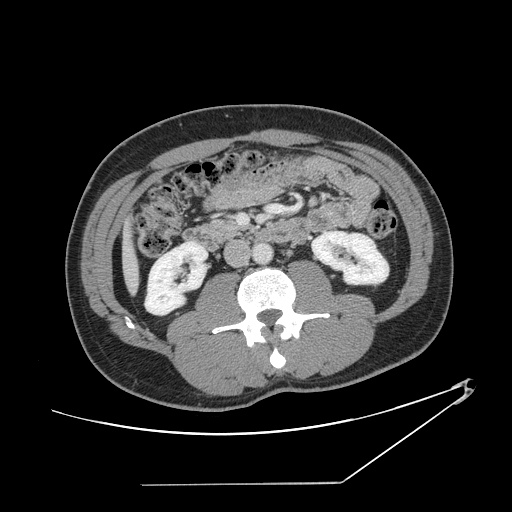
Contrast-enhanced abdominal CT, one axial slice; slice 43 of 152 in the series (ordered by position); reconstruction kernel STANDARD; intravenous contrast given; soft-tissue window (W 400 / L 40 HU); 2.5 mm slice thickness; 512 × 512 image matrix, field of view 432 × 432 mm. Male patient, age 45 years. Case-level facts recorded for this patient, not image findings: diagnosis: colorectal cancer liver metastases, imaged before liver resection; multiple liver metastases: no; largest metastasis: 1 cm.
Outlined on this slice (expert manual segmentation):
- liver: bounding box (x1, y1, x2, y2) in pixels: (124, 237, 138, 290)
- planned liver remnant (the part of the liver to remain after resection): (124, 238, 138, 290)